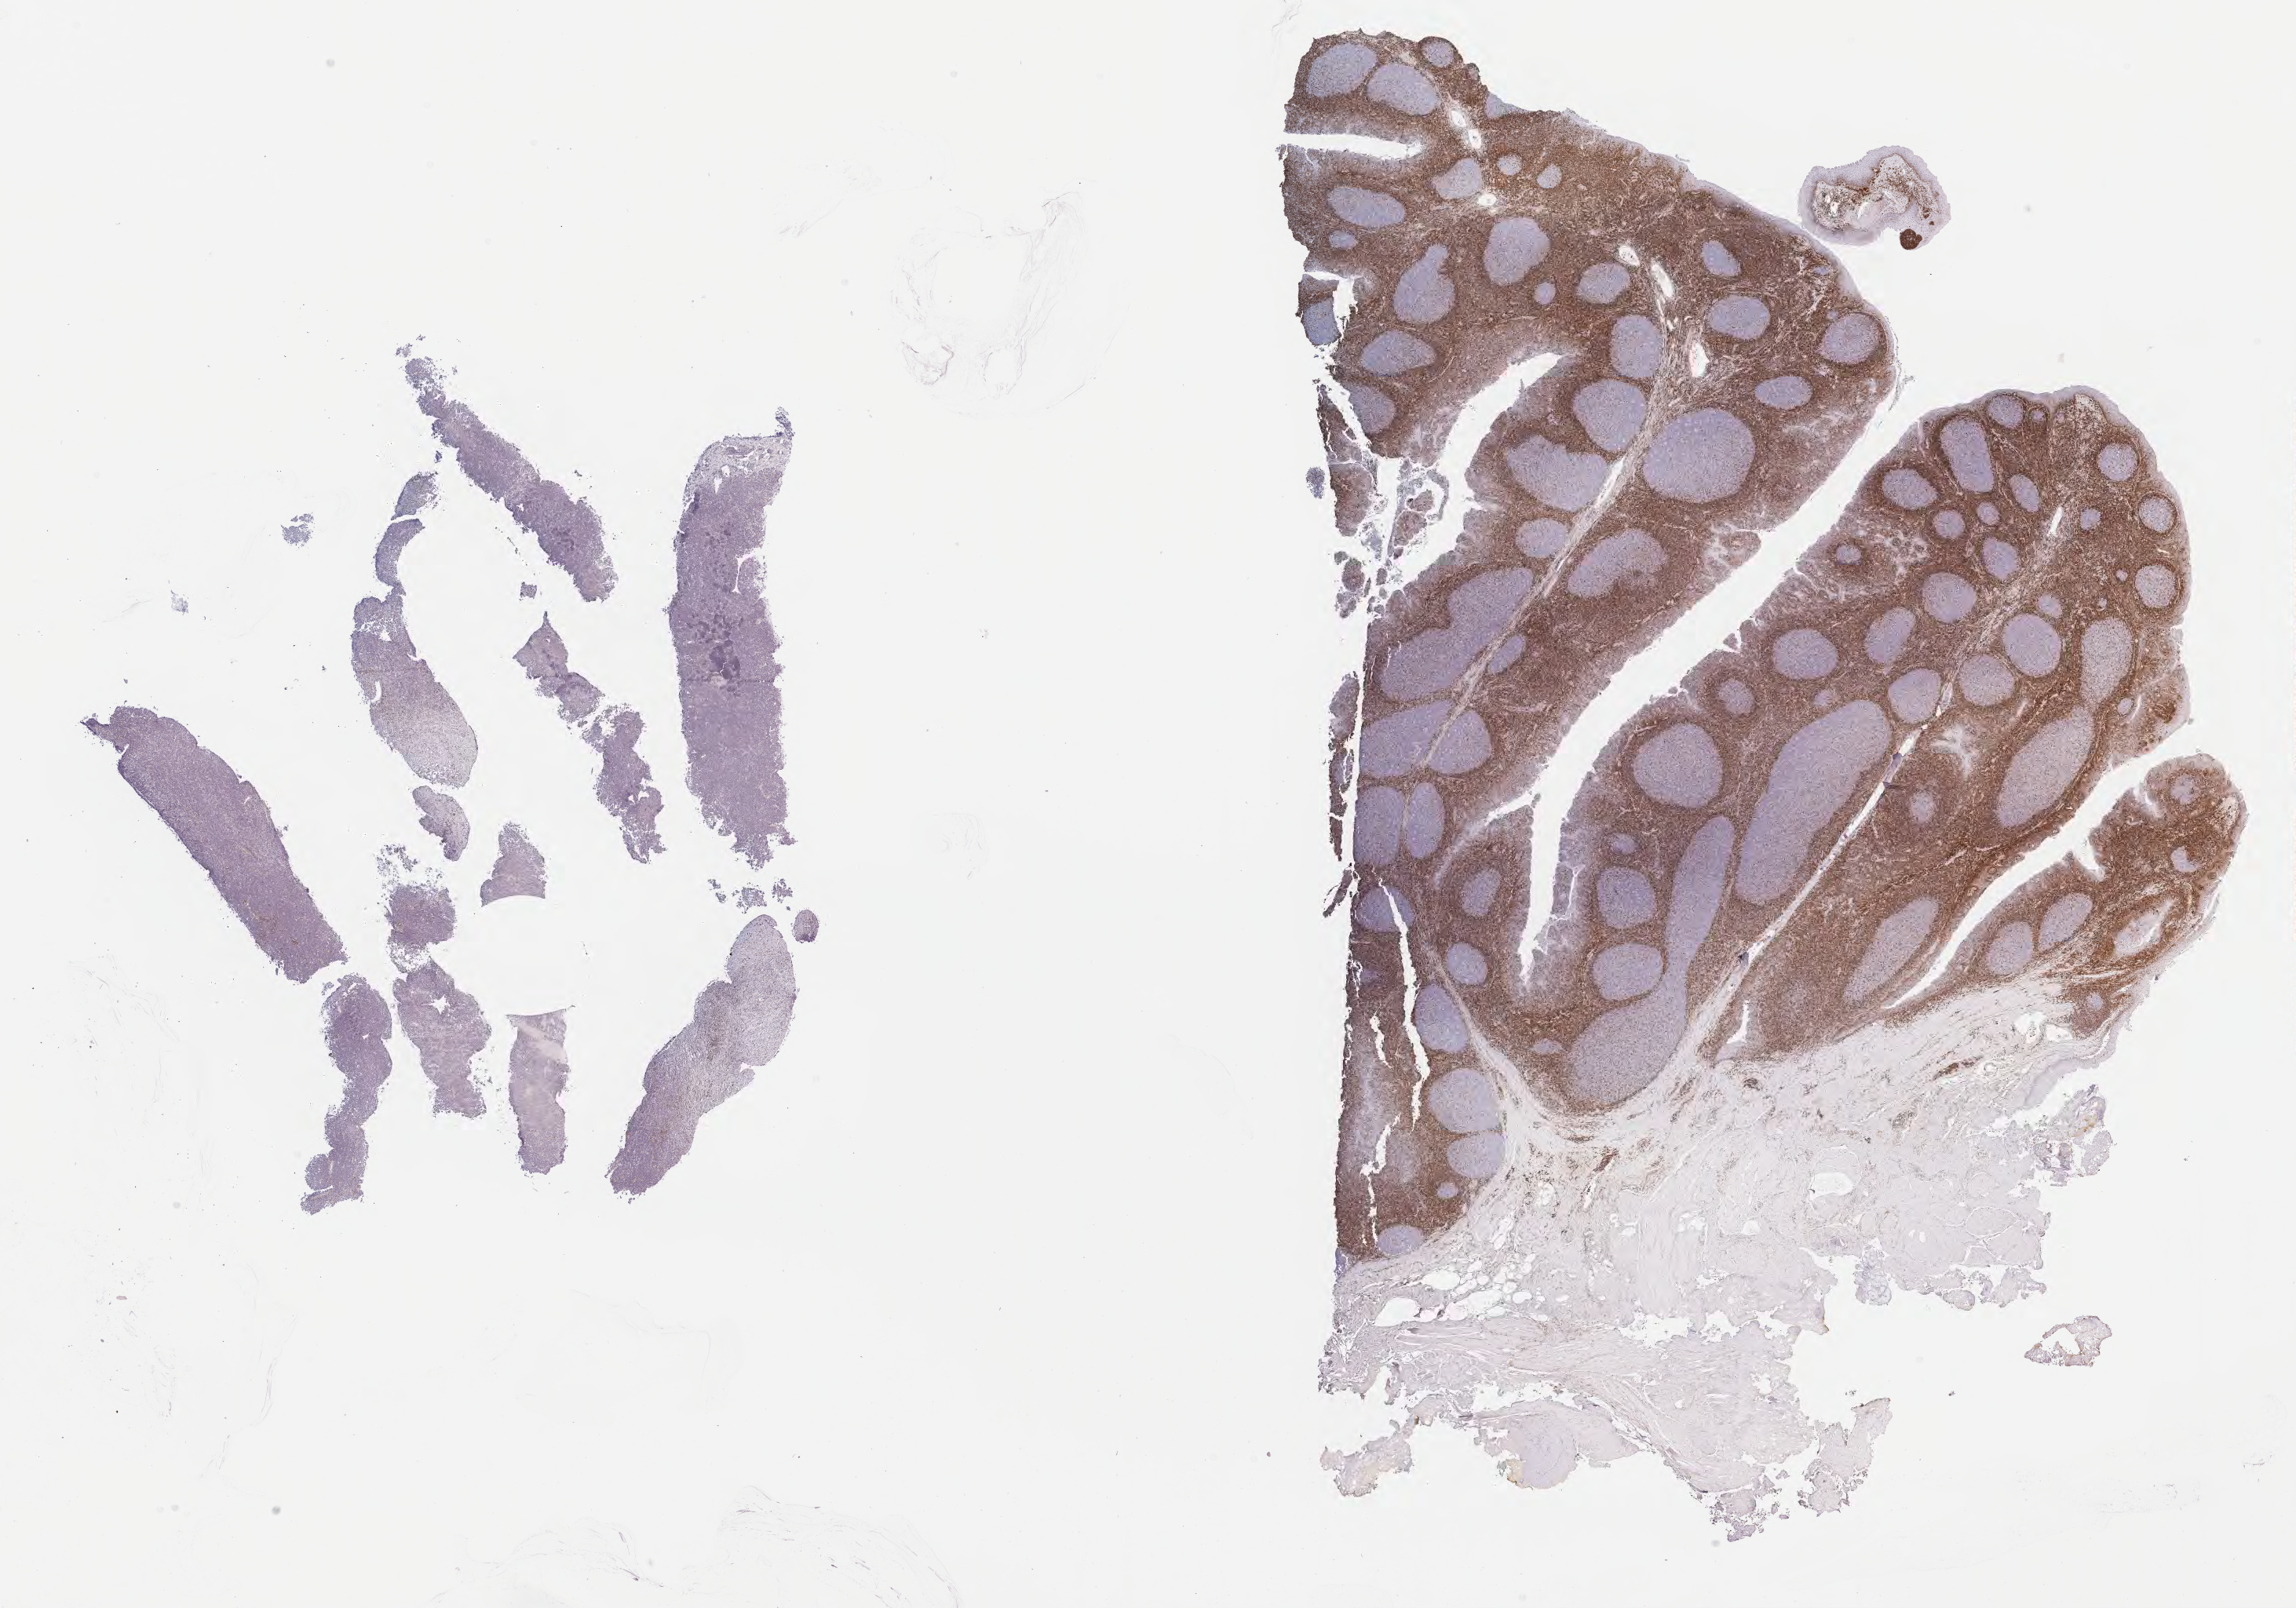
Immunohistochemistry (IHC) whole-slide image stained for BCL2 — a low-resolution overview of the entire scanned area, about 23.7 x 16.6 mm, tumor tissue, site: abdomen proper. Male, age 7 years at initial diagnosis.
• histologic diagnosis: Burkitt lymphoma, NOS